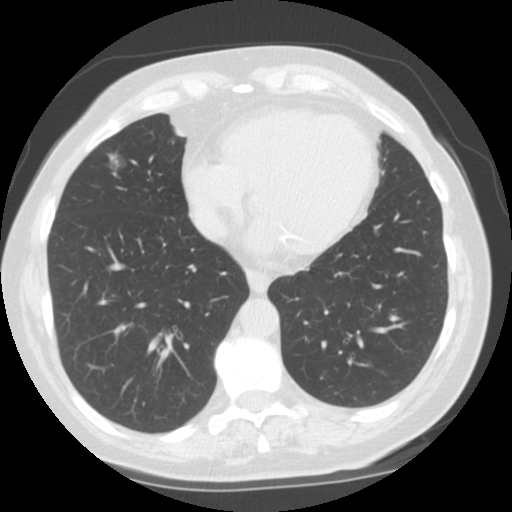
Axial slice from a low-dose chest CT screening exam. Baseline annual screen. Lung window (W 1500 / L -600 HU). Slice 35 of 112 in the series. 512 × 512 image matrix. Female, age 71 years at enrolment.
Expert reader's lesion annotation, bounding box [x1, y1, x2, y2] px = [84, 140, 140, 191]. The screening reader recorded 2 non-calcified nodules or masses ≥4 mm on this exam (right middle lobe, left upper lobe); which of them this box marks is not recorded. Official screen result: positive, change unspecified: nodule(s) >= 4 mm or enlarging nodule(s), mass(es), or other non-specific abnormalities suspicious for lung cancer. Participant outcome: lung cancer diagnosed 491 days after this screen (after the second annual screen) — adenocarcinoma, NOS, right middle lobe, moderately differentiated (G2), stage IA (AJCC 6th edition), 12 mm at pathology.